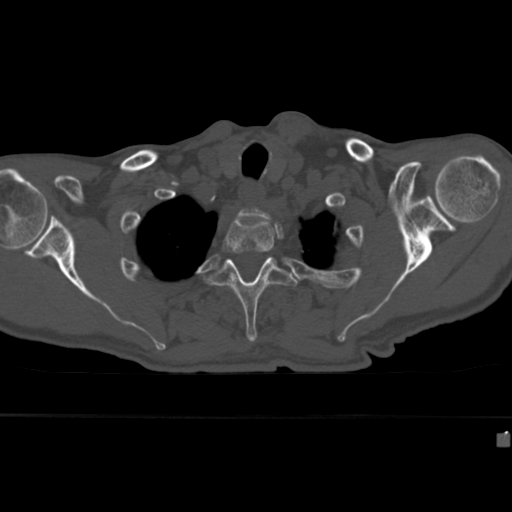
CT including the spine, one axial slice. Position 337 of 430 along the scan axis. 120 kVp. Bone window (W 1800 / L 400 HU). 512 × 512 image matrix. Patient: male, 64 years. Case-level facts recorded for this patient, not image findings: primary cancer: uterus; vertebrae with lytic lesions (as recorded): T1, T4, T5, T7, L5.
Outlined on this slice (semi-automatic segmentation, software-assisted and operator-edited):
- T2 vertebra: bounding box (x1, y1, x2, y2) in pixels: (222, 215, 293, 267)
- T3 vertebra: (206, 257, 299, 343)